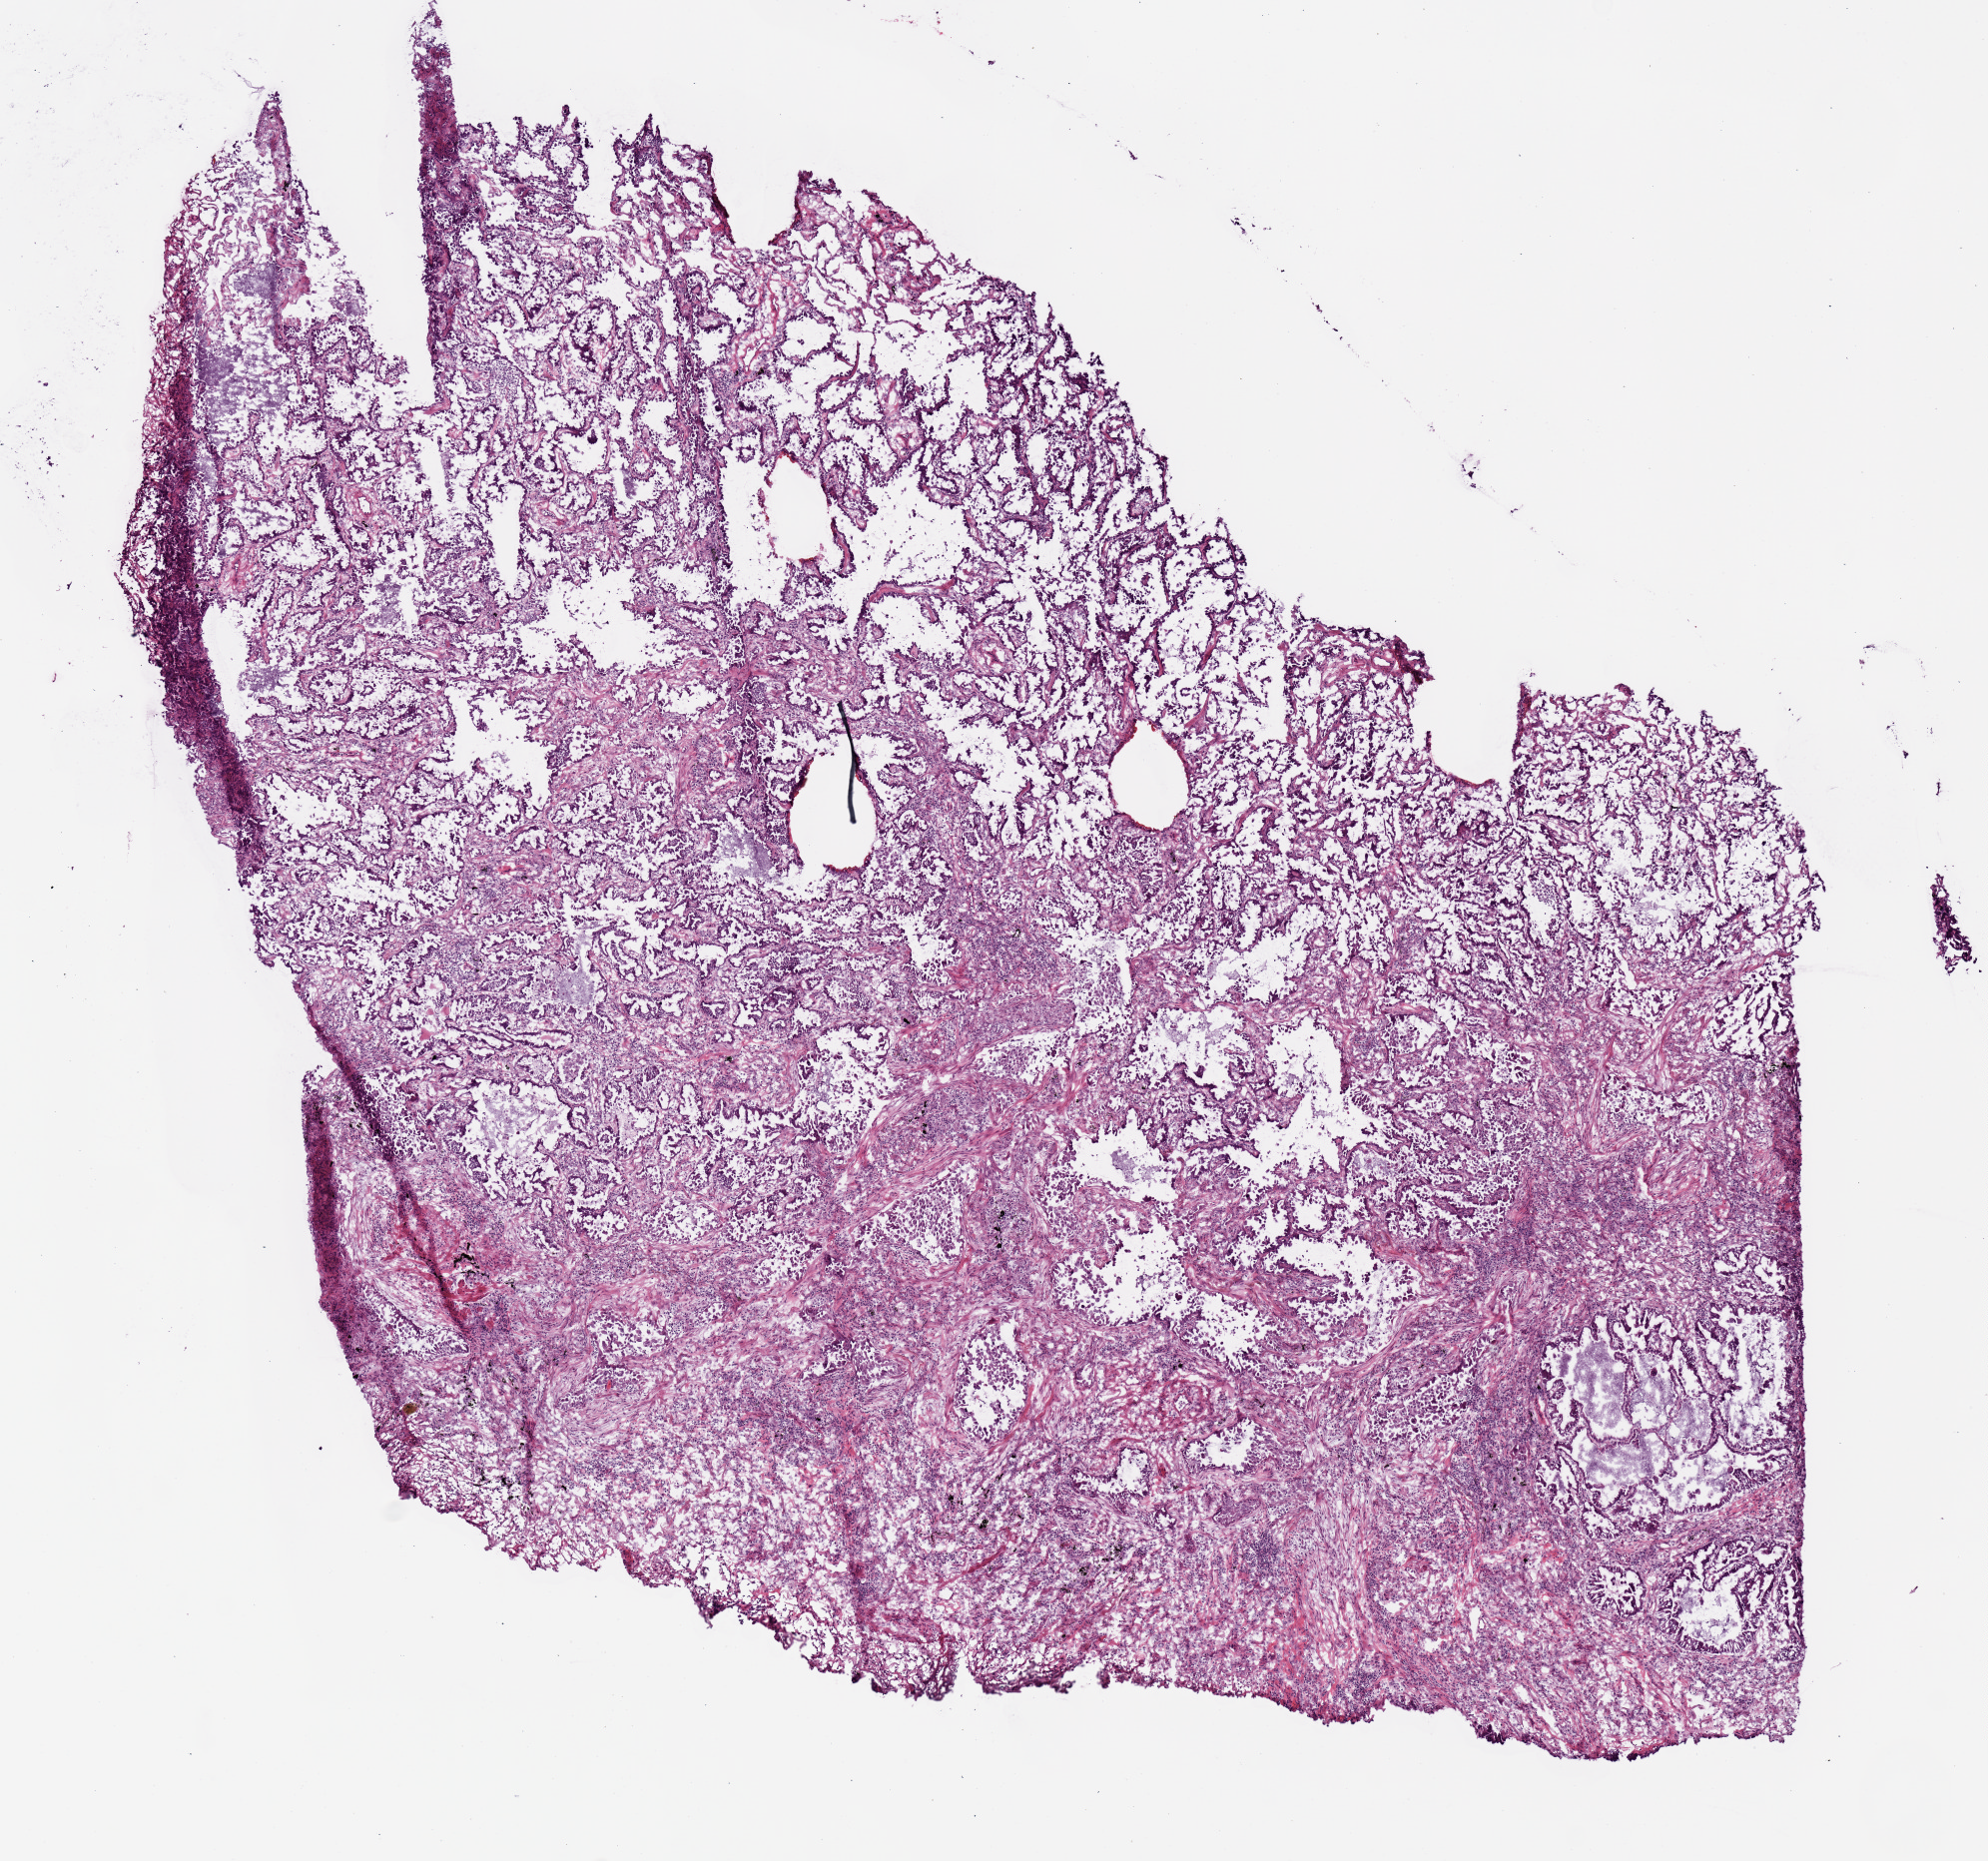
Whole-slide histology image, H&E — whole scanned area (about 7.9 x 7.4 mm) shown as a low-resolution overview, frozen section from the top of the tissue portion, sample: primary tumour, lung. Patient: female, age at initial diagnosis 76 years. Slide review estimates, as recorded: tumour cells 90%, tumour nuclei 65%, normal cells 0%, stromal cells 10%, necrosis 0%.
Pathologic diagnosis: Bronchiolo-alveolar carcinoma, non-mucinous (upper lobe, lung). AJCC pathologic stage: IIIA (7th edition).